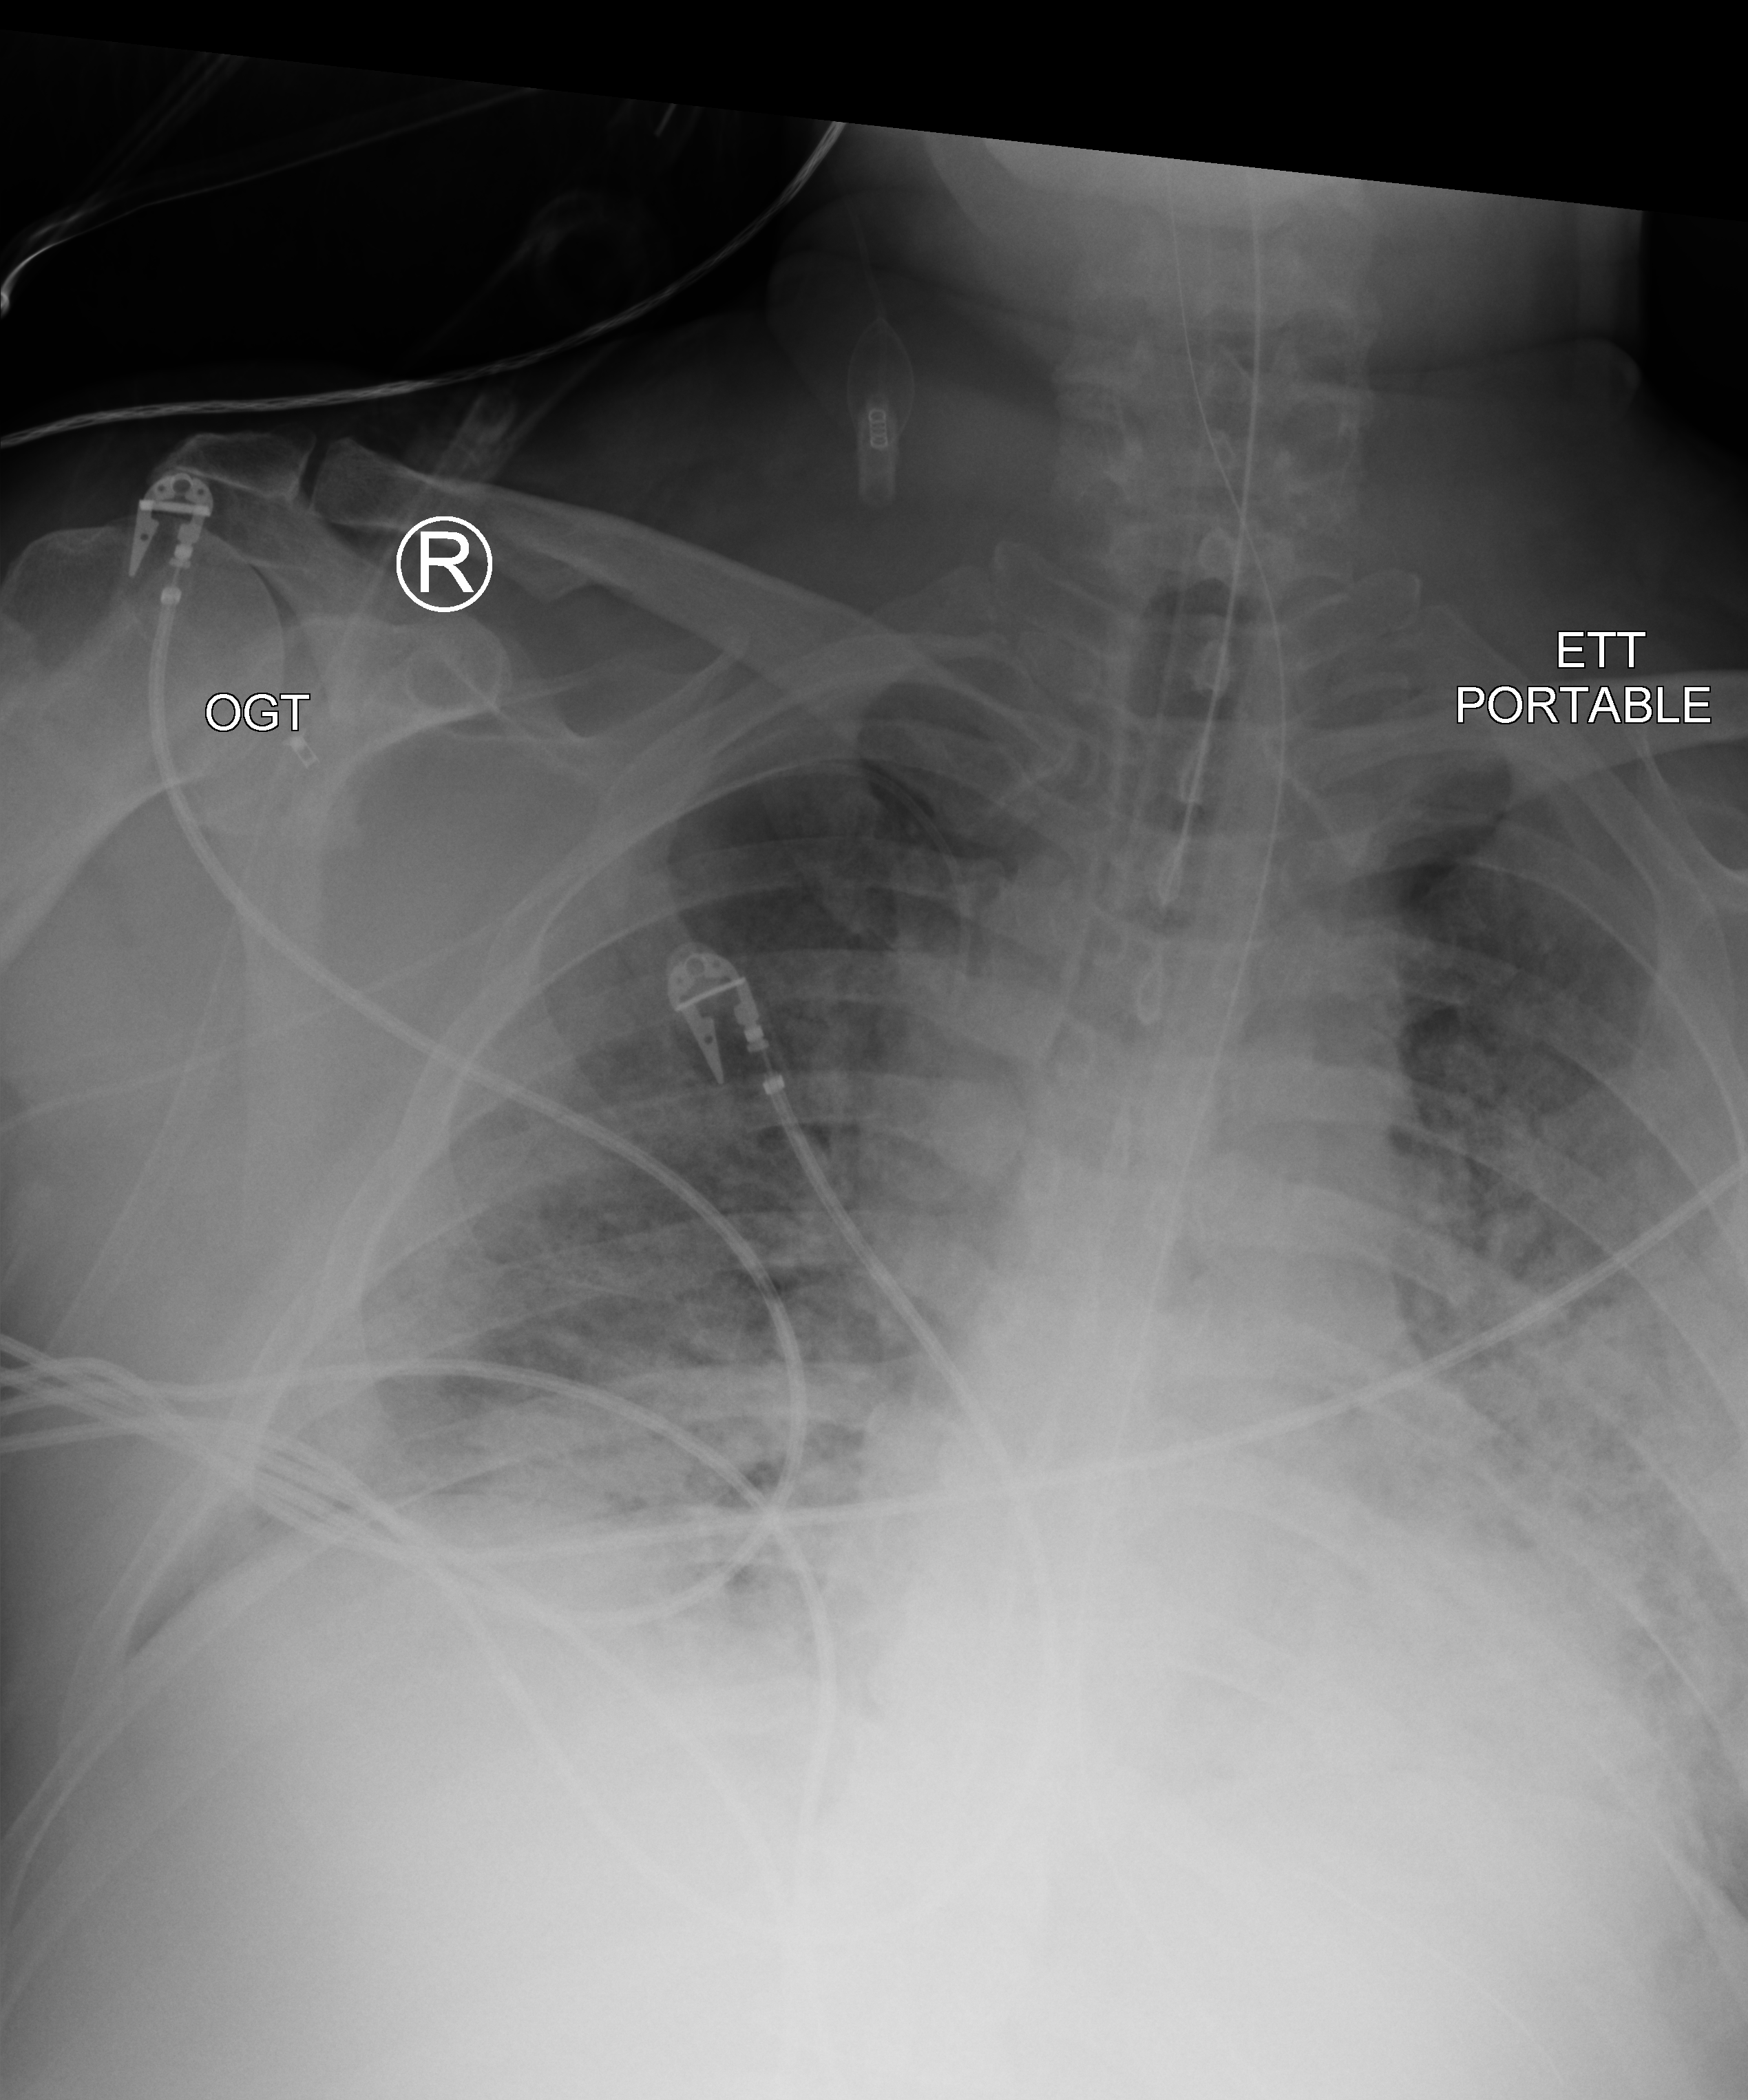
Bedside chest radiograph (computed radiography), anteroposterior (AP) projection. Male patient hospitalised with COVID-19, age 18–59 years.
Hospital-stay facts (about this admission, not read from this image; timing relative to this image not recorded): mechanically ventilated during this hospital stay: yes; admitted to intensive care during this hospital stay: yes.